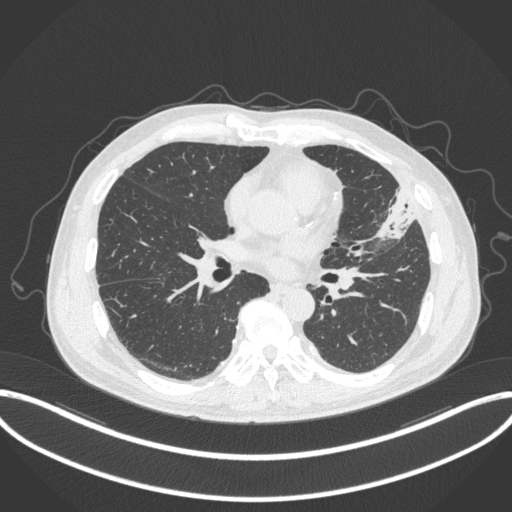
Chest CT, one axial slice; slice 161 of 382 in the series (ordered by position); reconstruction kernel B31f; lung window (W 1500 / L -600 HU); 512 × 512 image matrix, field of view 415 × 415 mm. Male patient, age 64 years. From the clinical record (not read from this slice): clinical TNM (as recorded): T4 N1 M0; histopathological grade: G3.
Structures marked on this image (rectangle marked by the reading radiologist):
- lung tumour (recorded histology: adenocarcinoma): box from (x=365, y=180) to (x=416, y=245) px